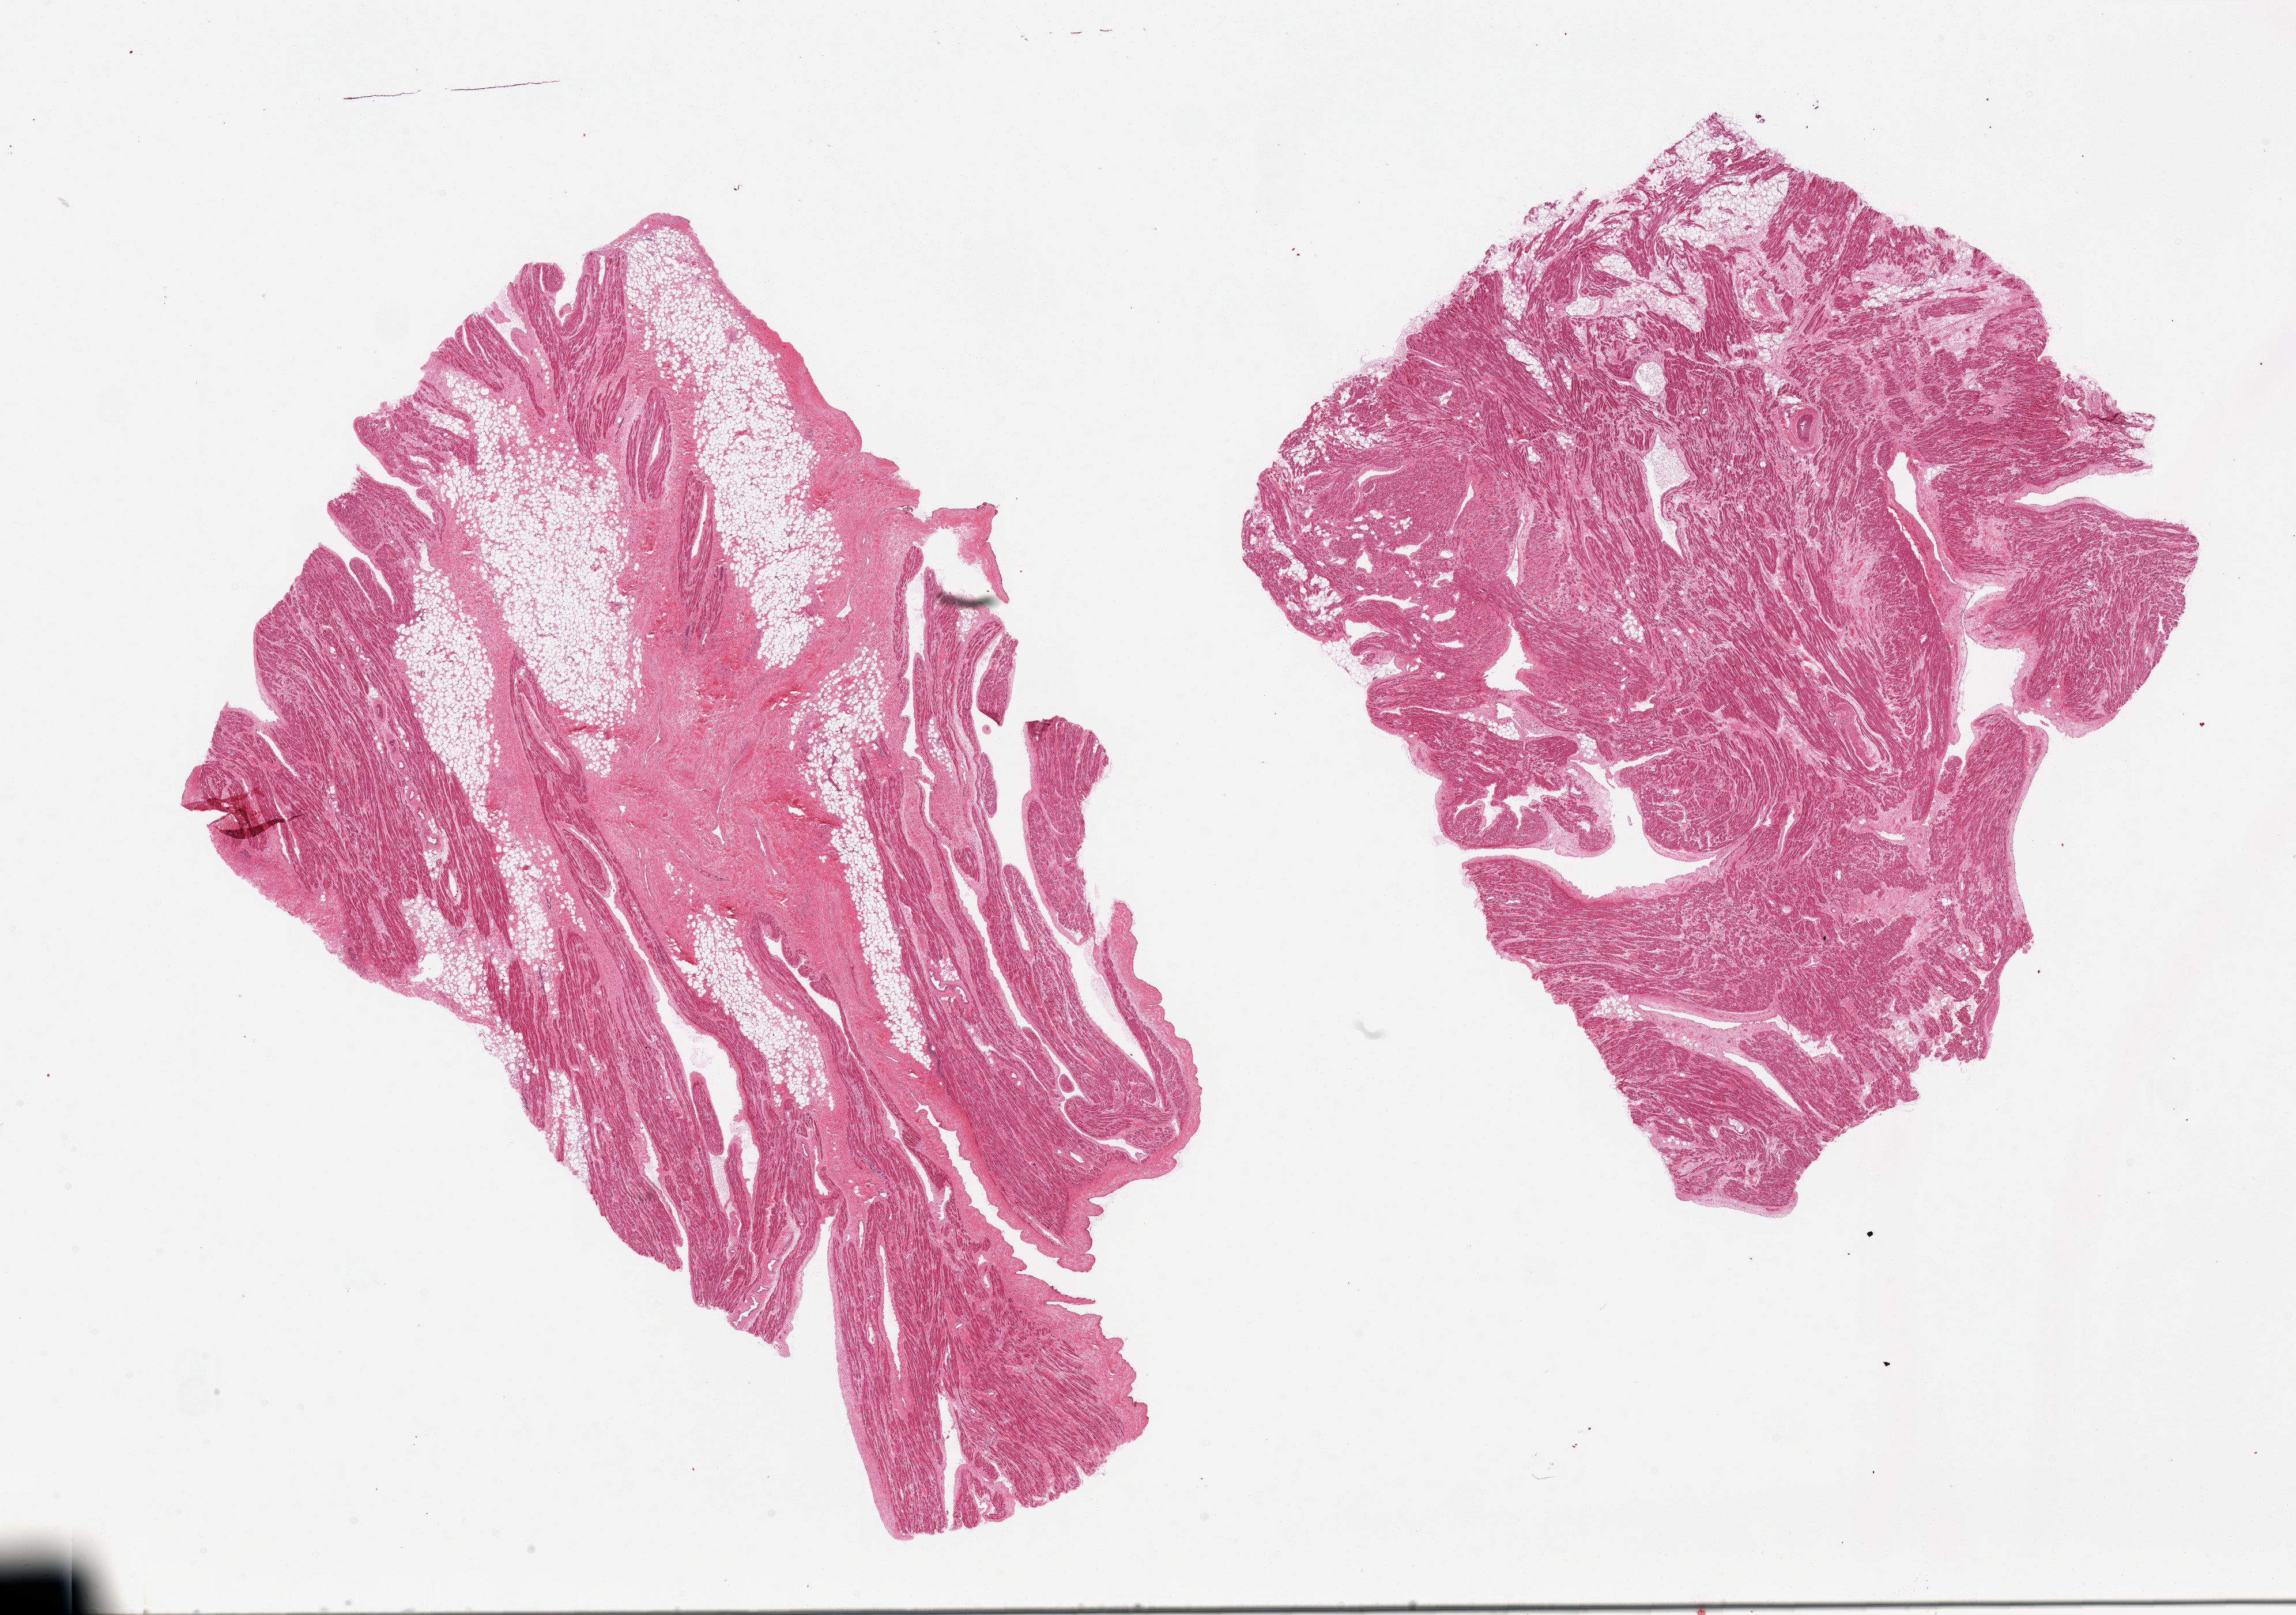
Hematoxylin and eosin (H&E) whole-slide image, brightfield — low-resolution overview of the scanned area, about 31.5 x 22.2 mm (from a 20x scan); PAXgene-fixed paraffin-embedded (PFPE) section; section of auricular appendage (target tissue); tissue donor sample. Donor: male.
- review note (as recorded): 2 pieces, 1 with 60% fibroadipose tissue